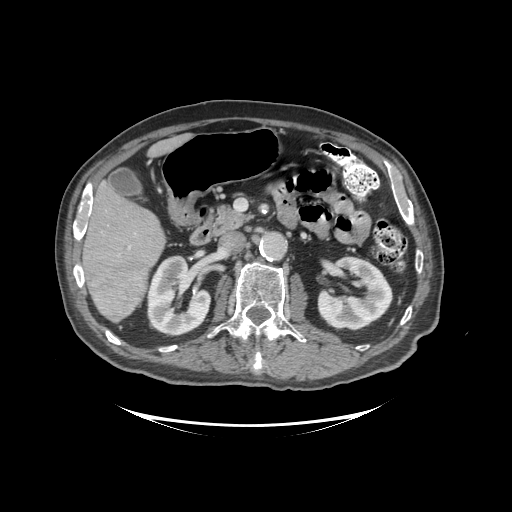
Contrast-enhanced abdominal CT (liver protocol), one axial slice; slice 45 of 99 in the series (ordered by position); reconstruction kernel STANDARD; soft-tissue window (W 400 / L 40 HU); 2.5 mm slice thickness; 512 × 512 image matrix, field of view 460 × 460 mm. Case-level facts recorded for this patient, not image findings: diagnosis: hepatocellular carcinoma (patient treated with transarterial chemoembolisation; whether this scan precedes or follows treatment is not stated here); TNM stage (as recorded): Stage-I; Child-Pugh class: A; tumour differentiation: moderately differentiated.
Structures marked on this image (semi-automatic segmentation, software-assisted and operator-edited):
- liver parenchyma outside the tumour (the mass and vessels are separate outlines, so this box may not span the whole liver): bounding box (x1, y1, x2, y2) in pixels: (82, 136, 186, 322)
- mass: (87, 259, 147, 317)
- liver vessels: (84, 200, 131, 248)